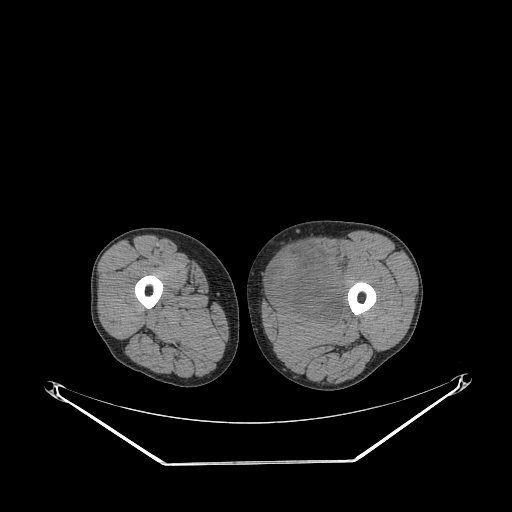
CT of an extremity soft-tissue mass (from a PET/CT study), one axial slice; slice 236 of 267 in the series (ordered by position); reconstruction kernel STANDARD; 140 kVp; soft-tissue window (W 400 / L 40 HU); 512 × 512 image matrix, field of view 500 × 500 mm. Male patient. Case-level facts recorded for this patient, not image findings: histological type: pleiomorphic liposarcoma; grade: high; site of the primary tumour: left thigh.
Outlined on this slice (expert contour drawn on MRI and transferred to this co-registered scan by the dataset authors):
- gross tumour volume including surrounding oedema: bounding box <269,240,352,320> (left, top, right, bottom; pixels)
- gross tumour volume (mass): <269,247,344,318>